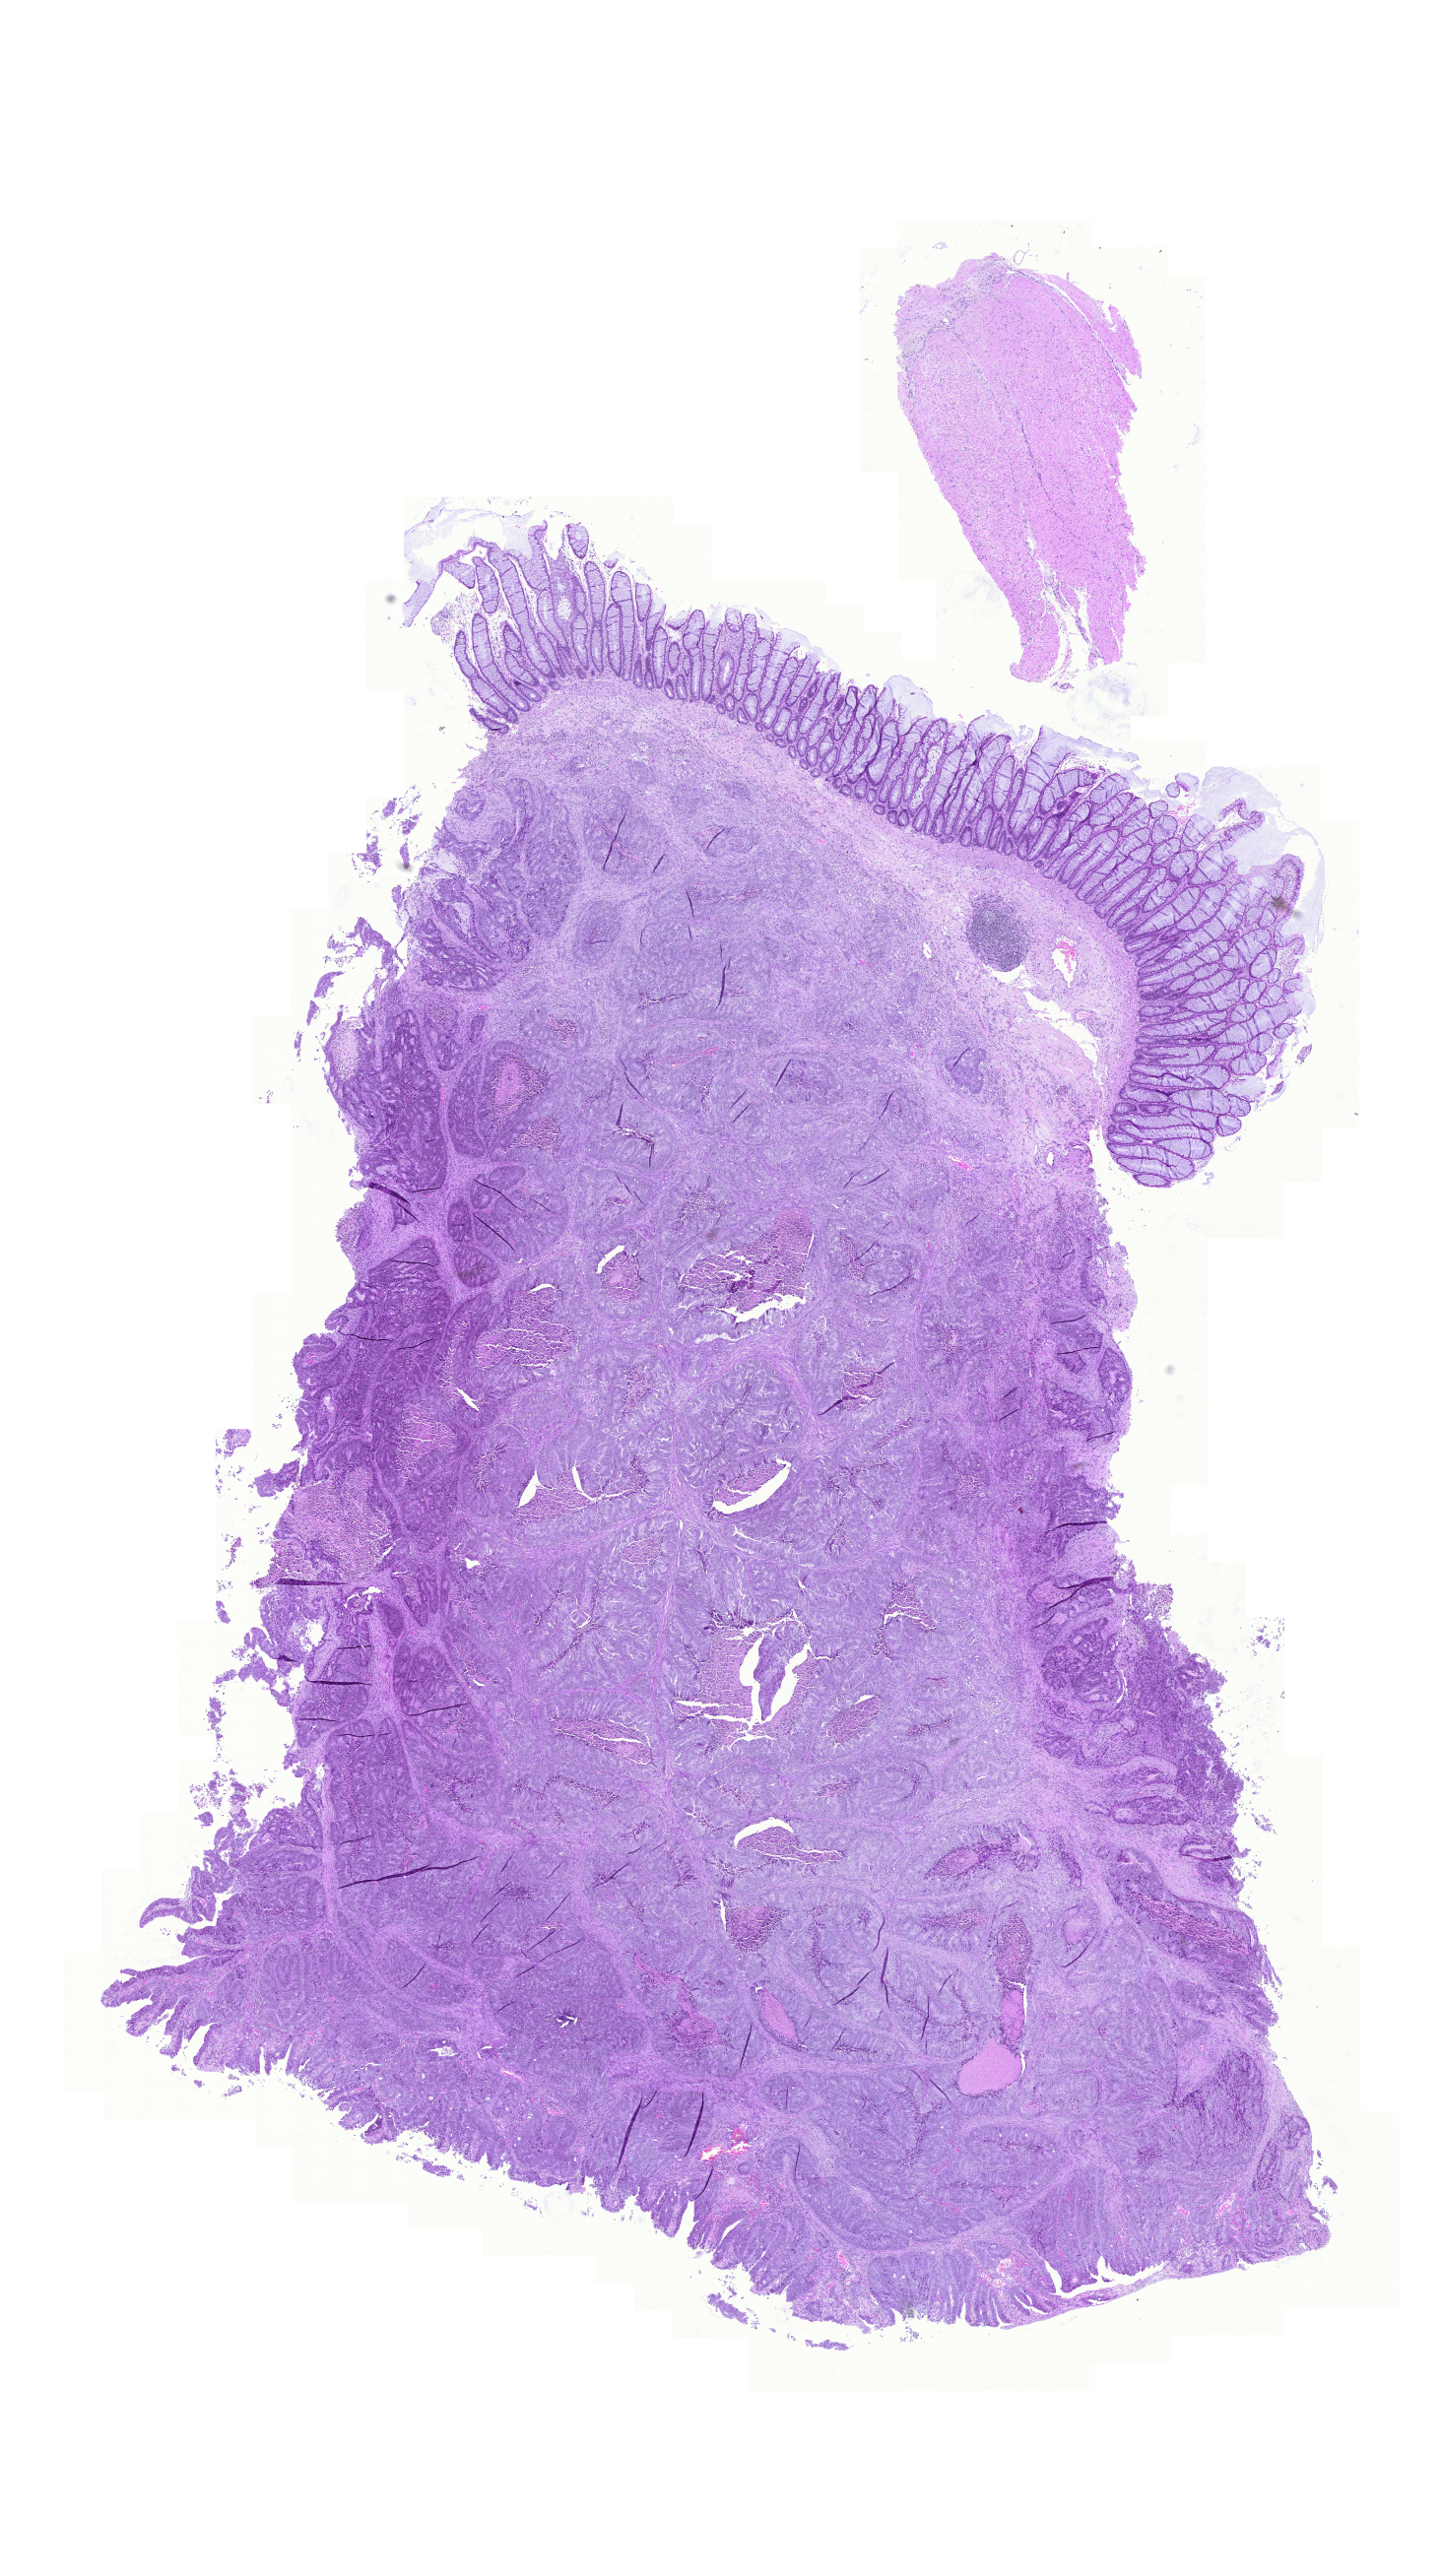
Digitized H&E tissue section (whole slide) — low-resolution overview of the scanned area, about 10.9 x 19.5 mm; formalin-fixed paraffin-embedded (FFPE) diagnostic section; colon, primary tumour sample. Female patient; age at initial diagnosis 47 years.
- TNM: T3 N1 M0
- AJCC pathologic stage: III (5th edition)
- pathologic diagnosis: Adenocarcinoma, NOS (sigmoid colon)